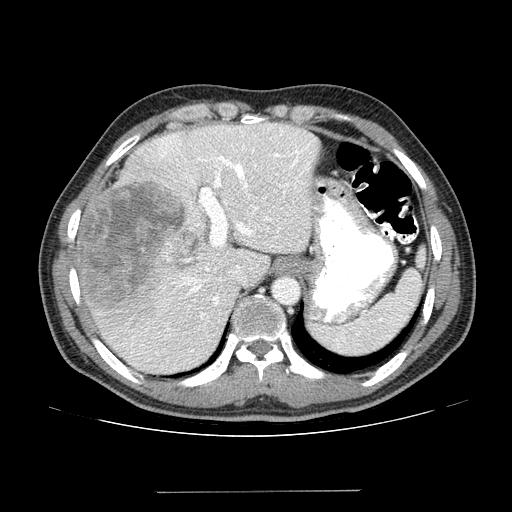
Contrast-enhanced abdominal CT (liver protocol), one axial slice; position 102 of 131 along the scan axis; 100 kVp; one of 2 acquisitions stored at this slice position; soft-tissue window (W 400 / L 40 HU); 512 × 512 image matrix, field of view 380 × 380 mm. From the clinical record (not read from this slice): diagnosis: hepatocellular carcinoma (patient treated with transarterial chemoembolisation; whether this scan precedes or follows treatment is not stated here); TNM stage (as recorded): Stage-I; Child-Pugh class: A; tumour differentiation: poorly differentiated; tumour nodularity: uninodular.
Structures marked on this image (semi-automatically segmented with operator editing):
- liver parenchyma outside the tumour (the mass and vessels are separate outlines, so this box may not span the whole liver): bounding box <74,122,318,372> (left, top, right, bottom; pixels)
- mass: <79,179,186,315>
- liver vessels: <131,125,315,362>